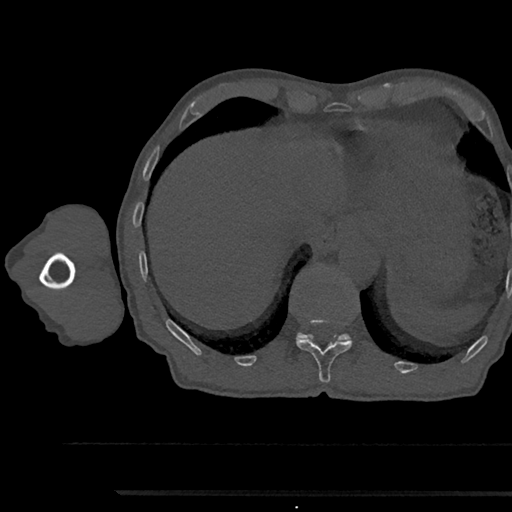
CT including the spine, one axial slice; position 764 of 797 along the scan axis; 120 kVp; bone window (W 1800 / L 400 HU); 0.5 mm slice thickness; 512 × 512 image matrix, field of view 367 × 367 mm. Patient: male, 79 years. From the clinical record (not read from this slice): primary cancer: prostate.
Outlined on this slice (semi-automatic segmentation, software-assisted and operator-edited):
- T11 vertebra: bounding box [x1, y1, x2, y2] px = [296, 338, 352, 383]
- T12 vertebra: [296, 332, 351, 341]